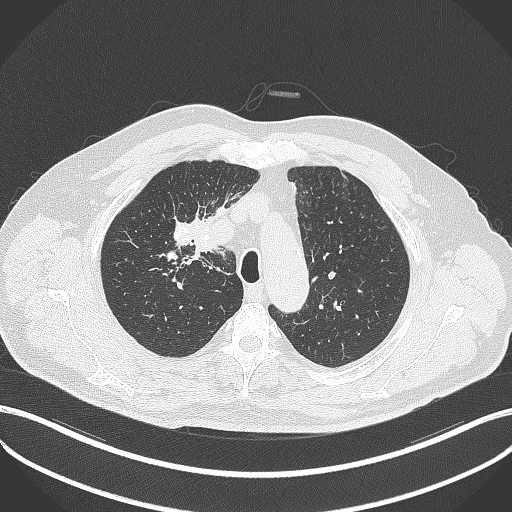
Chest CT, one axial slice; slice 302 of 411 in the series (ordered by position); reconstruction kernel B70f; lung window (W 1500 / L -600 HU); 1 mm slice thickness; 512 × 512 image matrix, field of view 400 × 400 mm. Patient: male, 60 years. From the clinical record (not read from this slice): clinical TNM (as recorded): T1b N1 M0.
Annotated regions visible in this slice (rectangle marked by the reading radiologist):
- lung tumour (recorded histology: squamous cell carcinoma): box from (x=184, y=224) to (x=228, y=257) px